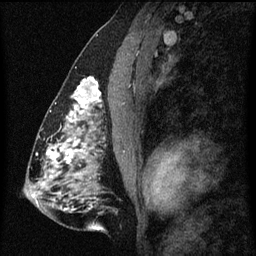
Breast MRI (dynamic contrast-enhanced), one sagittal slice. Position 33 of 60 along the scan axis. Dynamic contrast-enhanced series, image 2 of 3 at this slice position (ordered by acquisition). 1.5 T. TE 4.2 ms, TR 8 ms. 2 mm slice thickness. 256 × 256 image matrix. Patient: female, 51 years.
Outlined on this slice (semi-automatically segmented with operator editing):
- analysis volume of interest (the breast-tissue region the enhancement analysis was run in; not a lesion): bounding box [x1, y1, x2, y2] px = [61, 70, 102, 129]
- tumour enhancement mask (voxels above the 70 % enhancement threshold inside the analysis volume of interest): [66, 78, 102, 123]